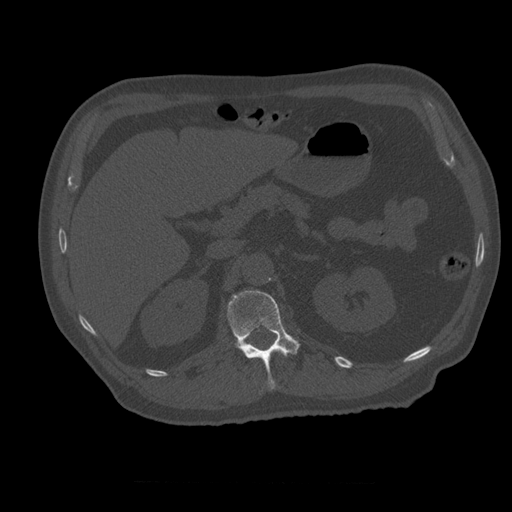
CT including the spine, one axial slice. Position 239 of 399 along the scan axis. 120 kVp. Bone window (W 1800 / L 400 HU). 1.25 mm slice thickness. 512 × 512 image matrix, field of view 407 × 407 mm. Patient age 73 years. Case-level facts recorded for this patient, not image findings: primary cancer: prostate.
Structures marked on this image (semi-automatically segmented with operator editing):
- L1 vertebra: bounding box (x1, y1, x2, y2) in pixels: (228, 290, 300, 390)
- T12 vertebra: (283, 354, 288, 357)